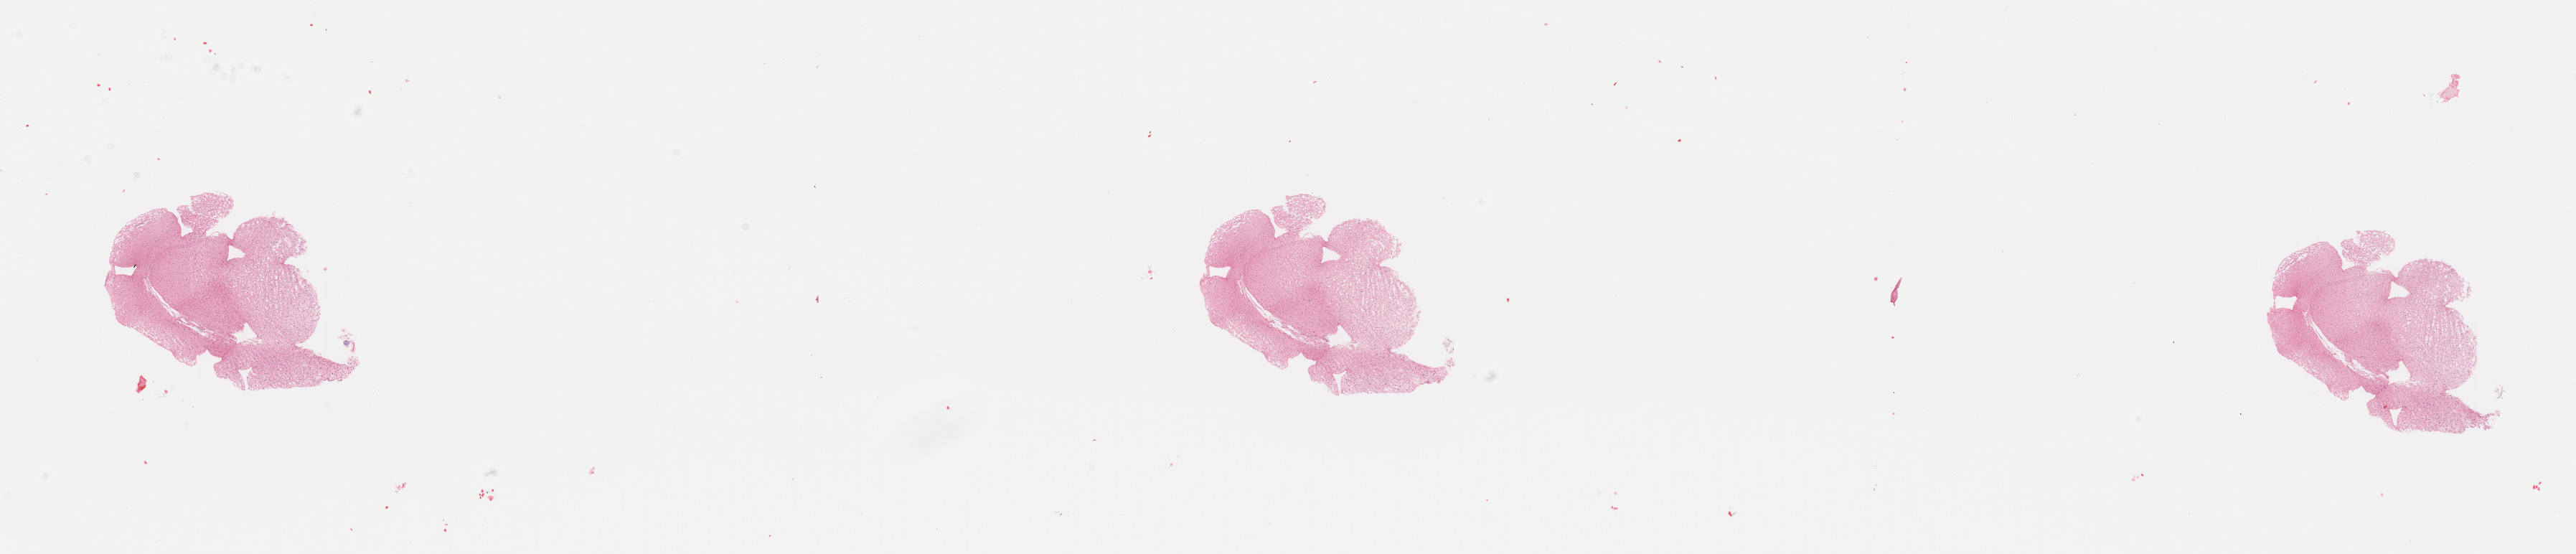
Digitized H&E tissue section (whole slide) — a low-resolution overview of the entire scanned area, about 28.6 x 6.1 mm, frozen section from the top of the tissue portion, brain, primary tumour sample. Patient: male, age at initial diagnosis 31 years. Histologic grade: G2 (moderately differentiated). Composition of this section per pathologist review: tumour cells 45%, tumour nuclei 70%, normal cells 10%, stromal cells 45%, necrosis 0%. Infiltration values recorded for this section: lymphocyte infiltration 0%, monocyte infiltration 0%, neutrophil infiltration 0%.
• pathologic diagnosis: Mixed glioma (cerebrum)